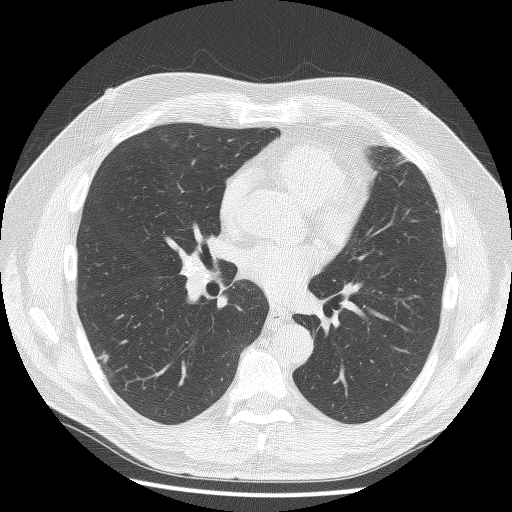
Low-dose screening chest CT, axial slice; baseline annual screen; lung window (W 1500 / L -600 HU); 2.5 mm slice thickness; lung (sharp) reconstruction kernel (BONE); 120 kVp; 512 × 512 image matrix, field of view 375 × 375 mm. Male participant, aged 61 years at enrolment. Former smoker at enrolment.
Lesion marked by an expert reader, box from (x=77, y=336) to (x=126, y=387) px. Screening reader's record for this exam (one nodule recorded; not confirmed to be the boxed lesion): non-calcified nodule or mass ≥4 mm, right lower lobe, 10 × 8 mm, spiculated (stellate) margins, soft tissue attenuation. Lung cancer was diagnosed 407 days after this screen: adenosquamous carcinoma, right lower lobe, poorly differentiated (G3), stage IV (AJCC 6th edition), 45 mm at pathology.